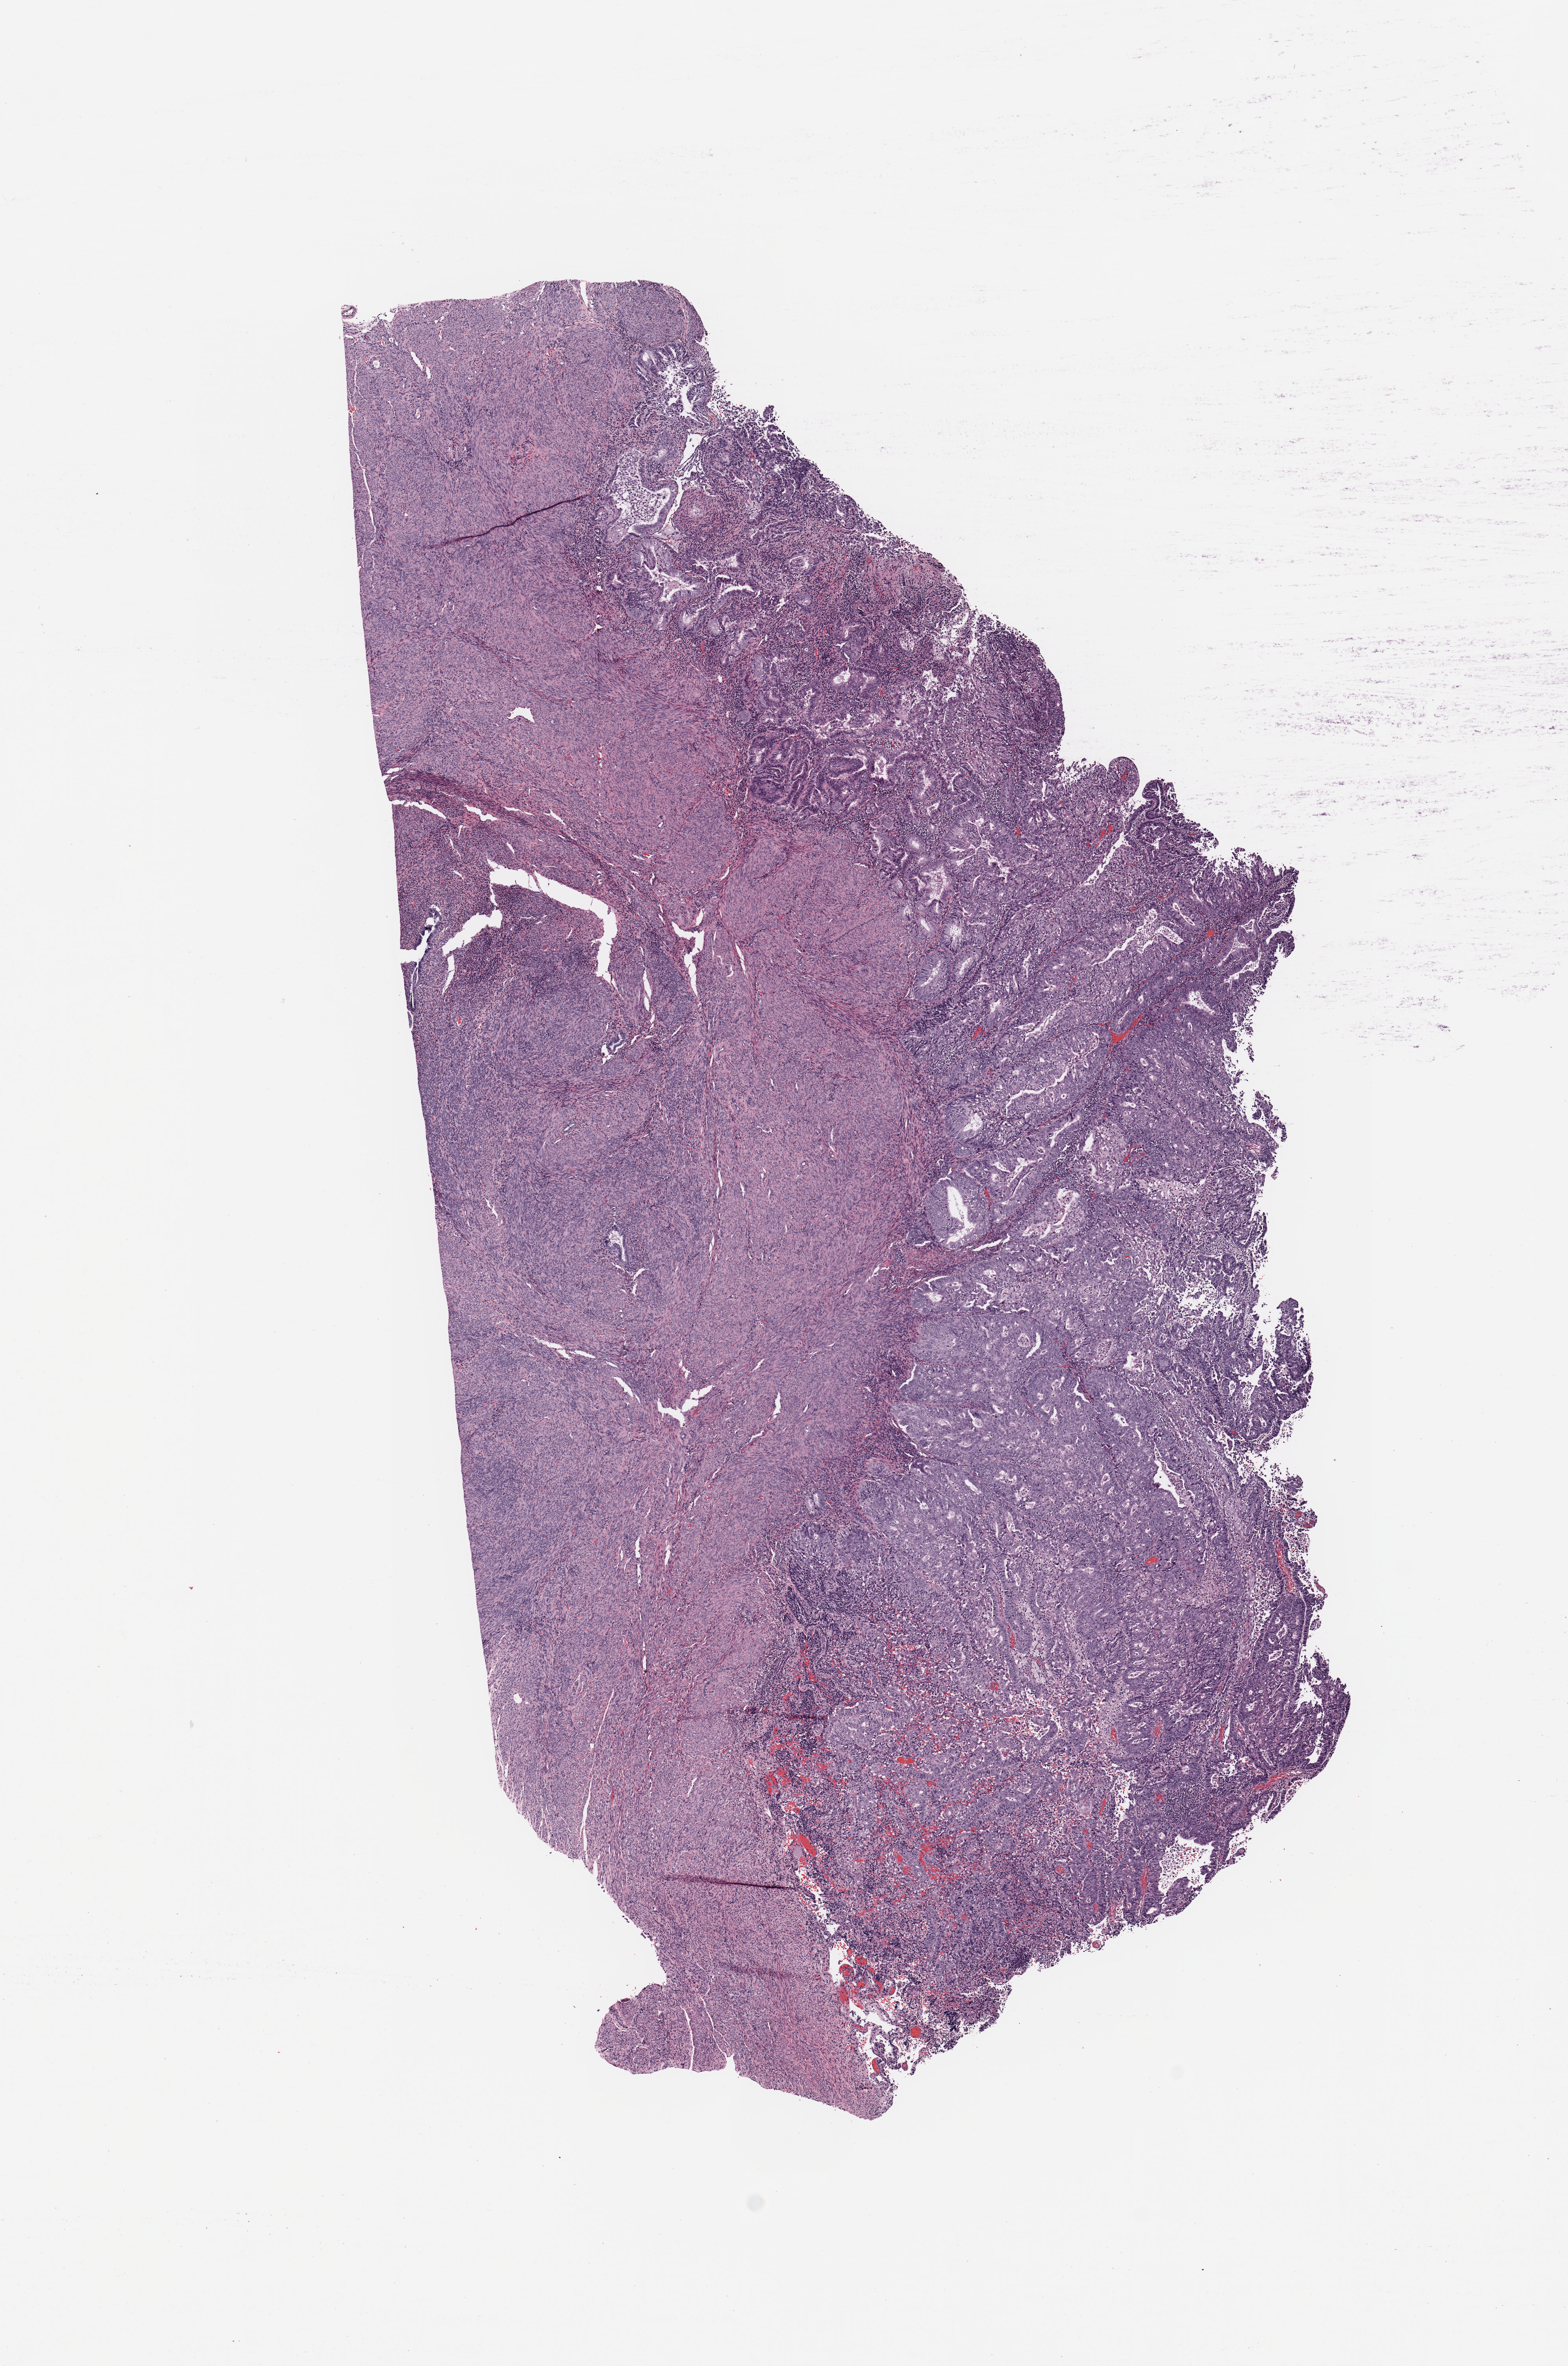
Whole-slide histology image, H&E-stained, low-resolution overview of the scanned area, about 7.9 x 11.9 mm. Tumour tissue sample, sampled site: uterus. Female, 77 y/o. Histologic grade: G2 (moderately differentiated). Pathologist review of this section (percent, as recorded): tumour nuclei 80%, necrosis 0%.
- AJCC pathologic stage: I
- diagnosis: Endometrioid adenocarcinoma, NOS